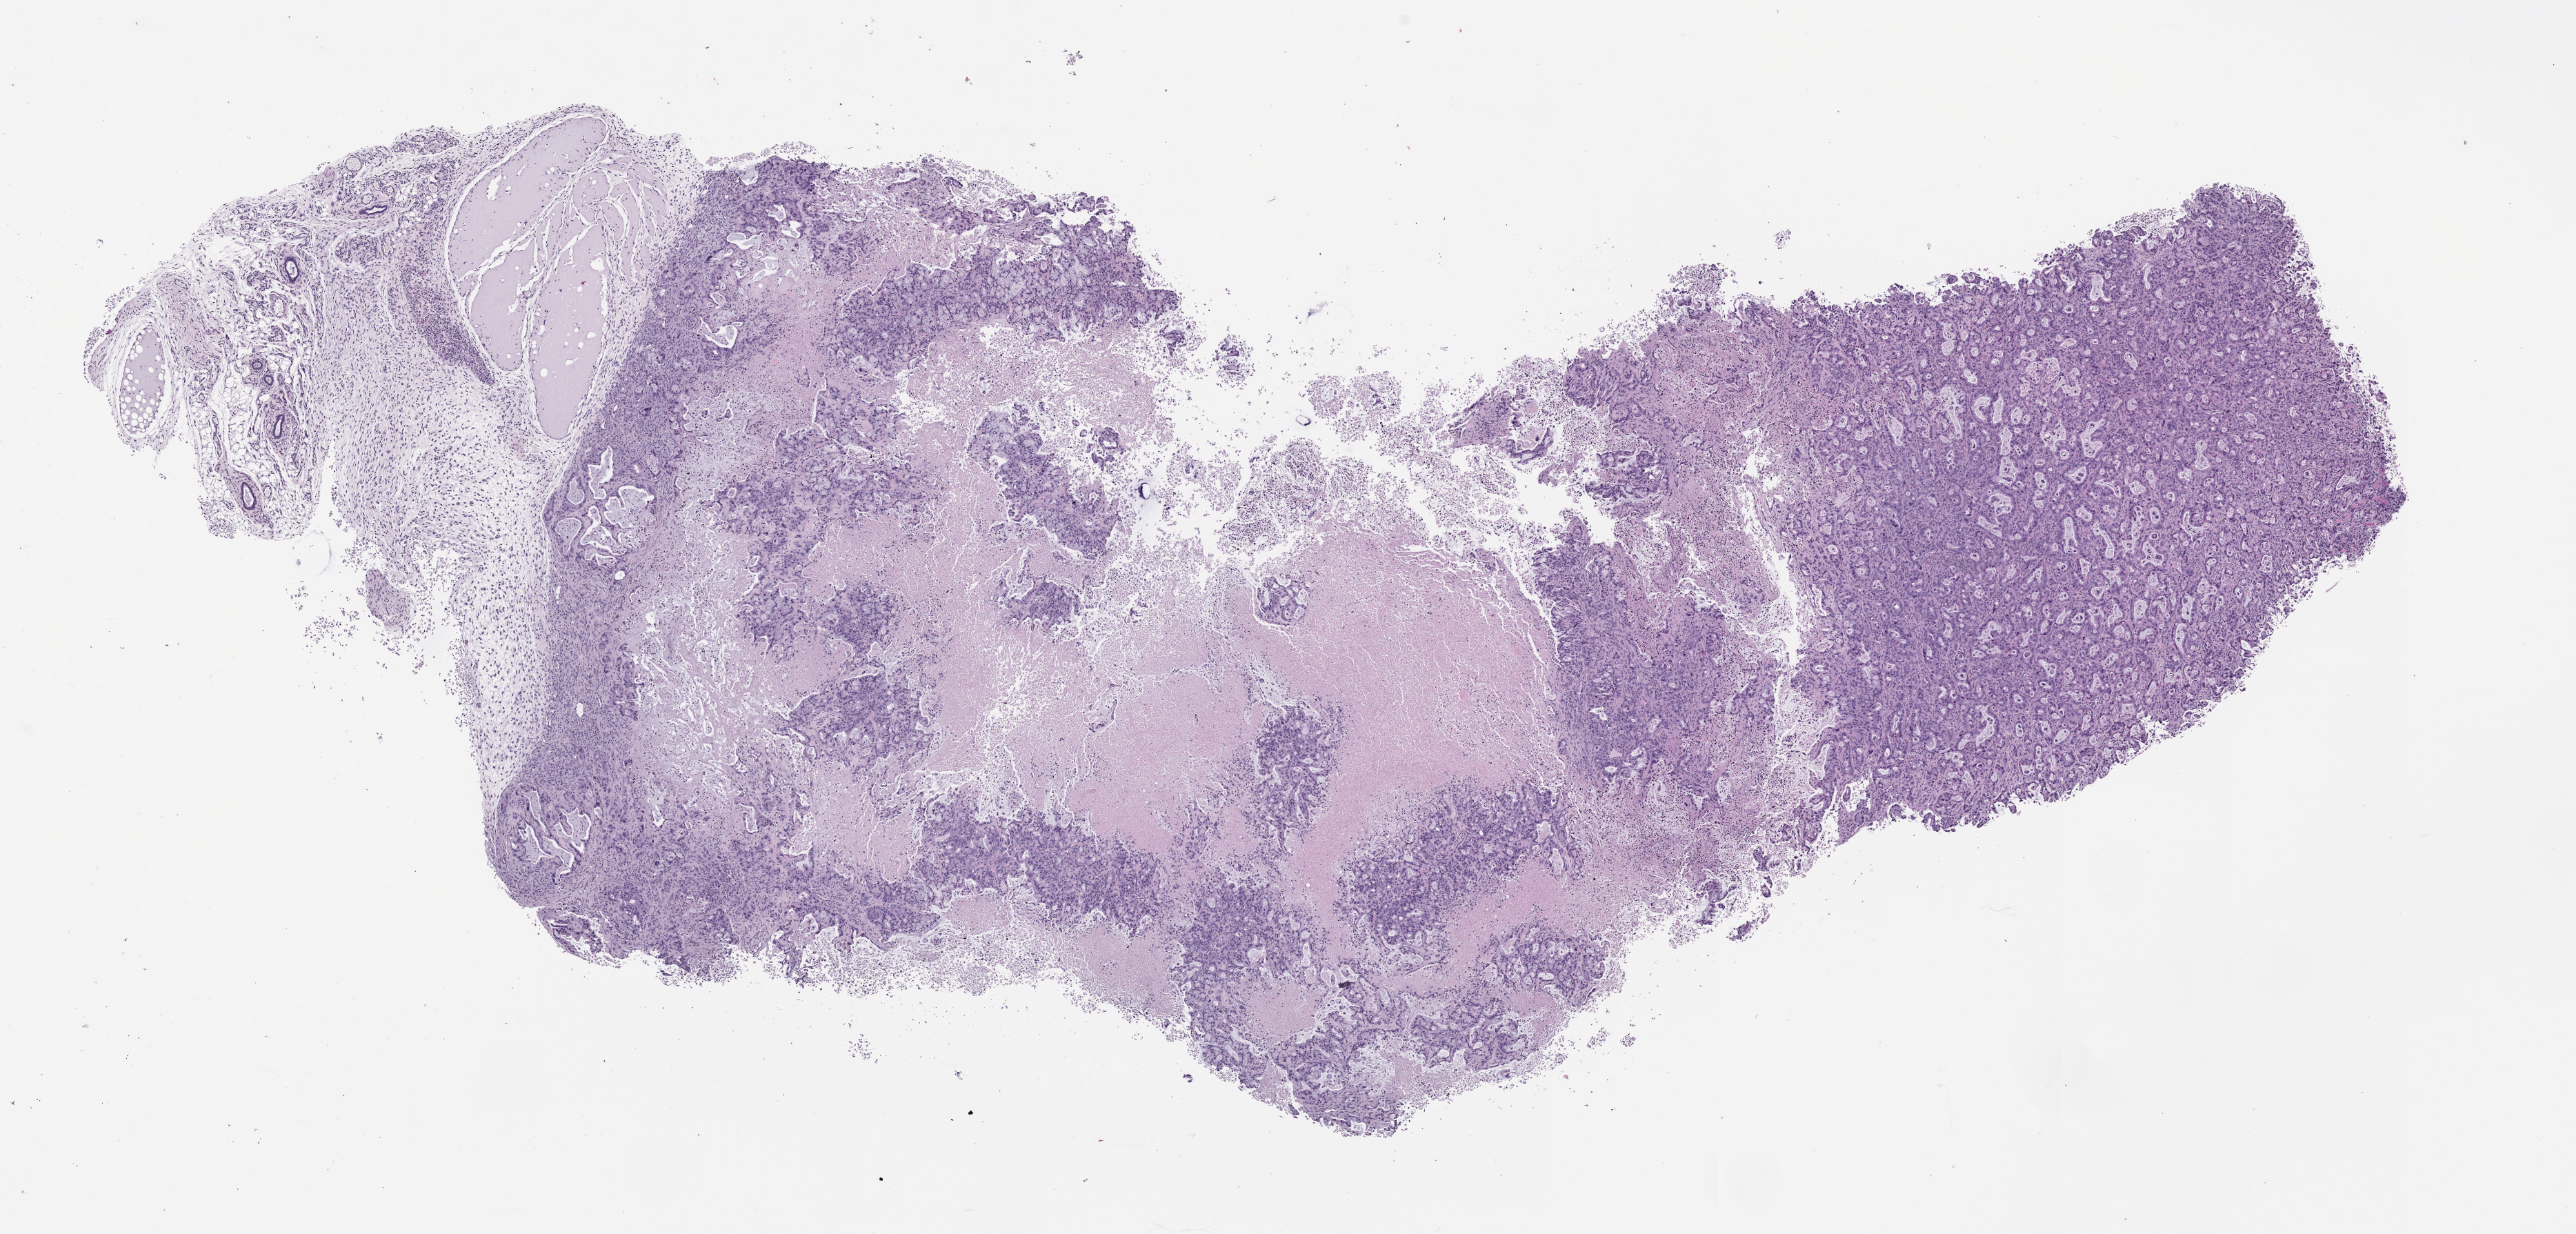
Whole-slide image, haematoxylin and eosin: patient-derived xenograft (human tumor grown in a mouse), passage 0, shown as a low-resolution overview of the whole scanned area (about 15.0 x 7.2 mm), formalin-fixed, paraffin-embedded (FFPE) tissue, tumor site category: pancreas.
Originating patient diagnosis: Pancreatic Adenocarcinoma.